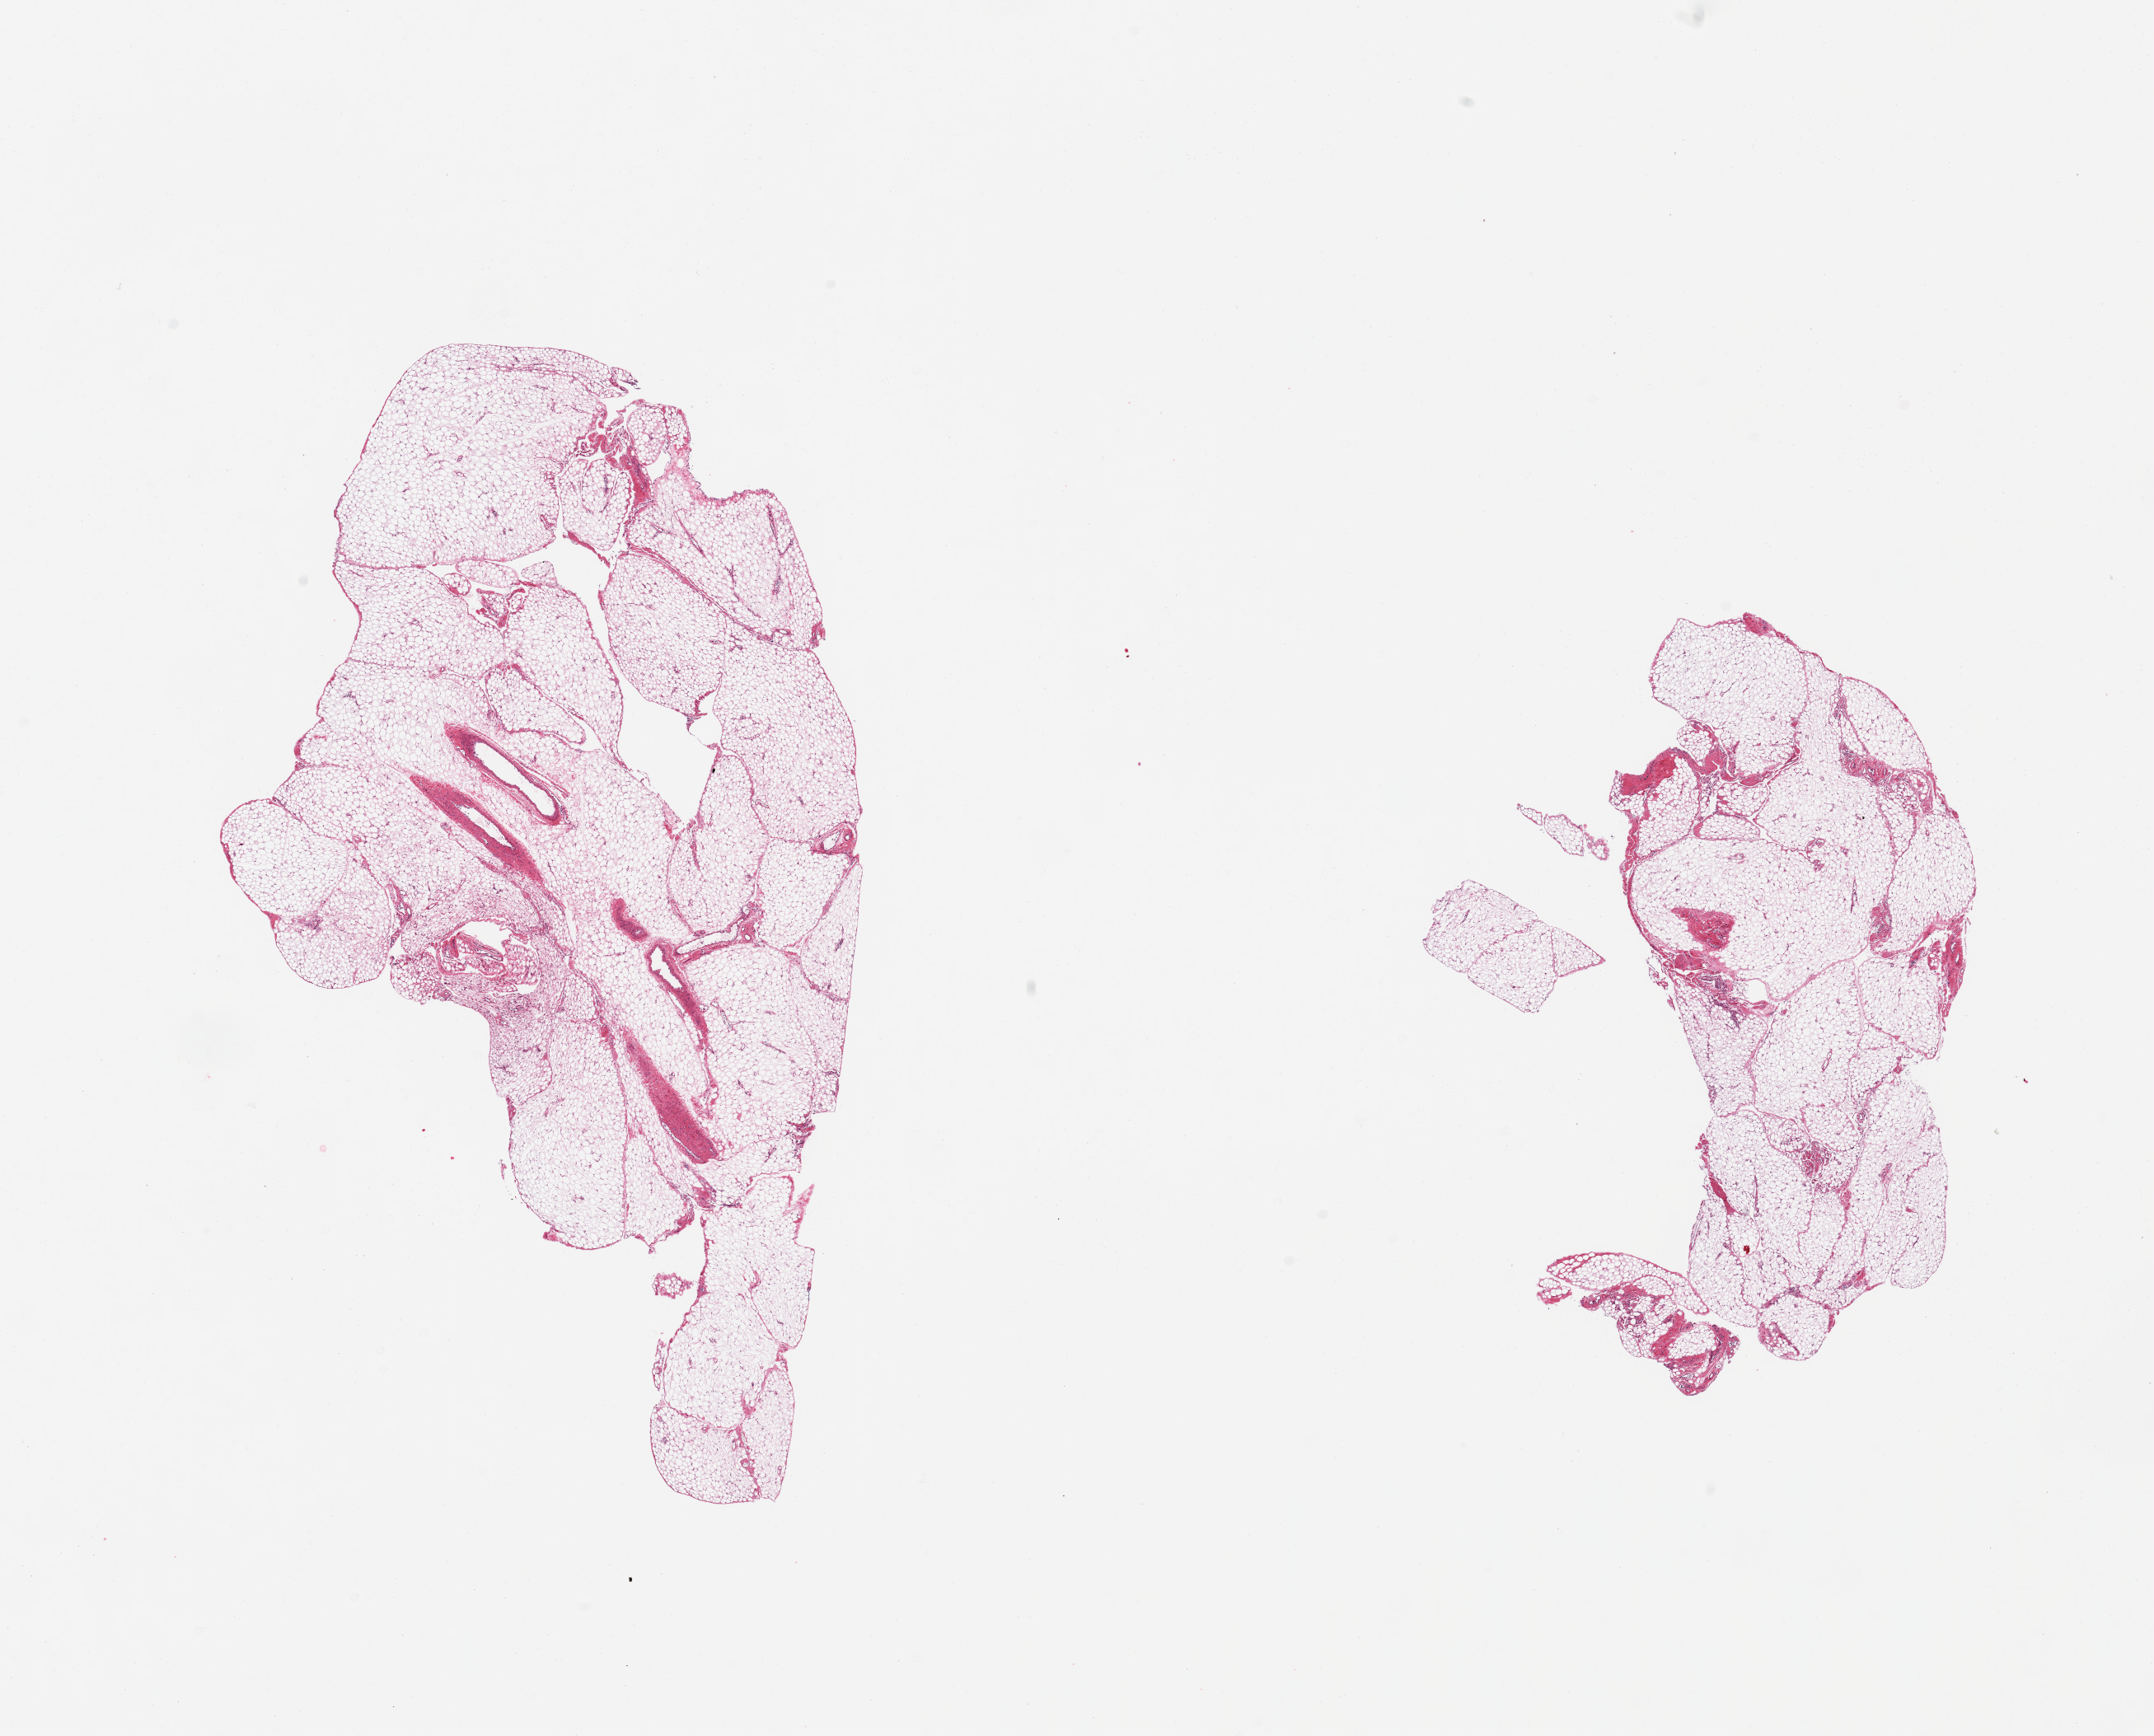
Whole-slide image, haematoxylin and eosin stain, brightfield, low-resolution overview of the scanned area, about 20.7 x 16.7 mm, PAXgene-fixed paraffin-embedded (PFPE) section, section of omentum (target tissue), tissue donor sample. Donor sex: male.
• review note (as recorded): 2 pieces; lobulated mature adipose tissue with fibrovascular component